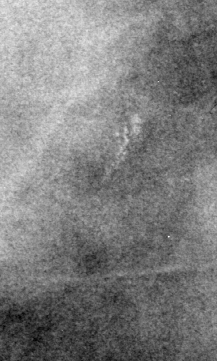
Region of interest cut from a scanned film mammogram (one marked finding); right breast; MLO view.
Finding: calcifications, morphology pleomorphic, distribution clustered; BI-RADS assessment category 4; subtlety rating 3 on a 1 (subtle) to 5 (obvious) scale; pathology result (as recorded, not read from the image): benign.